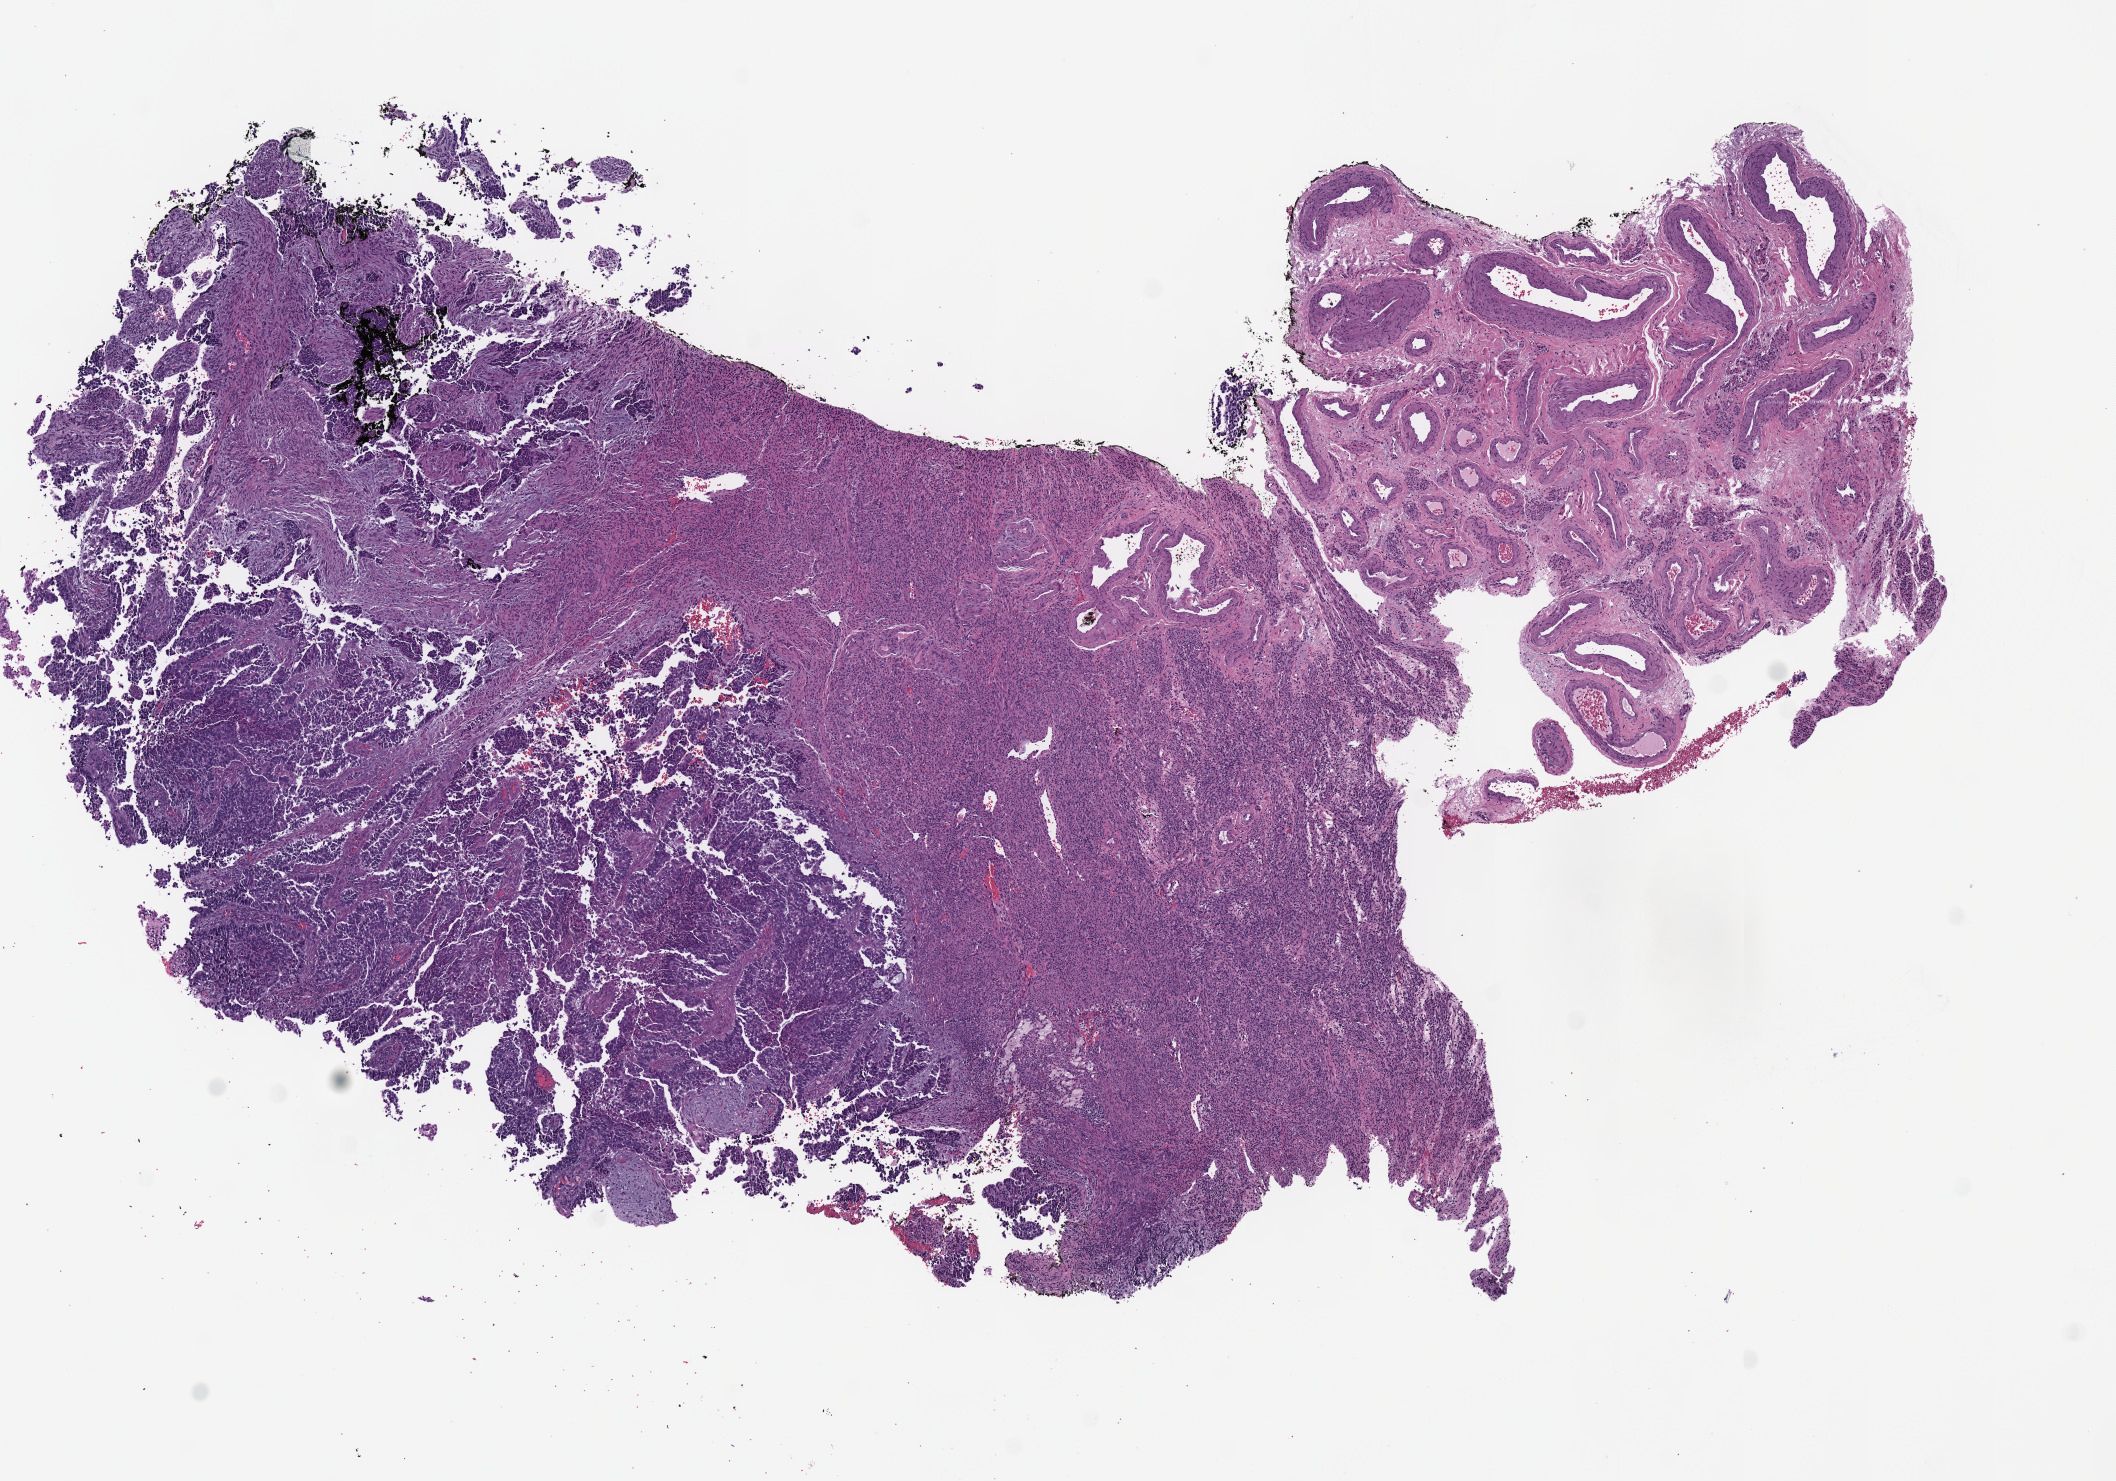
Digitized Hematoxylin and eosin (H&E) stained tissue section (whole slide), shown as a low-resolution overview of the whole scanned area (about 8.3 x 5.8 mm, acquisition: 40x scan). Formalin-fixed paraffin-embedded (FFPE) diagnostic section. Uterus, primary tumour sample. Patient: female, age at initial diagnosis 83 years. Histologic grade: G3 (poorly differentiated).
Diagnosis: Serous cystadenocarcinoma, NOS (endometrium). FIGO stage: II. Lymph nodes positive (case pathology): 0 of 7 examined.